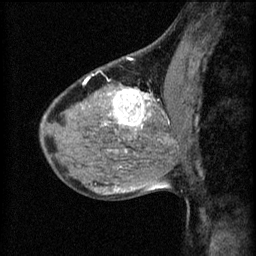
Breast MRI (dynamic contrast-enhanced), one sagittal slice; position 28 of 60 along the scan axis; 3 images stored at this slice position (order not interpretable as contrast timing); 1.5 T; TE 4.2 ms, TR 8.2 ms; 2.2 mm slice thickness; 256 × 256 image matrix, field of view 180 × 180 mm. Female patient, age 40 years.
Structures marked on this image (semi-automatic segmentation, software-assisted and operator-edited):
- analysis volume of interest (the breast-tissue region the enhancement analysis was run in; not a lesion): box from (x=108, y=82) to (x=175, y=139) px
- tumour enhancement mask (voxels above the 70 % enhancement threshold inside the analysis volume of interest): (x=108, y=88)–(x=171, y=131)